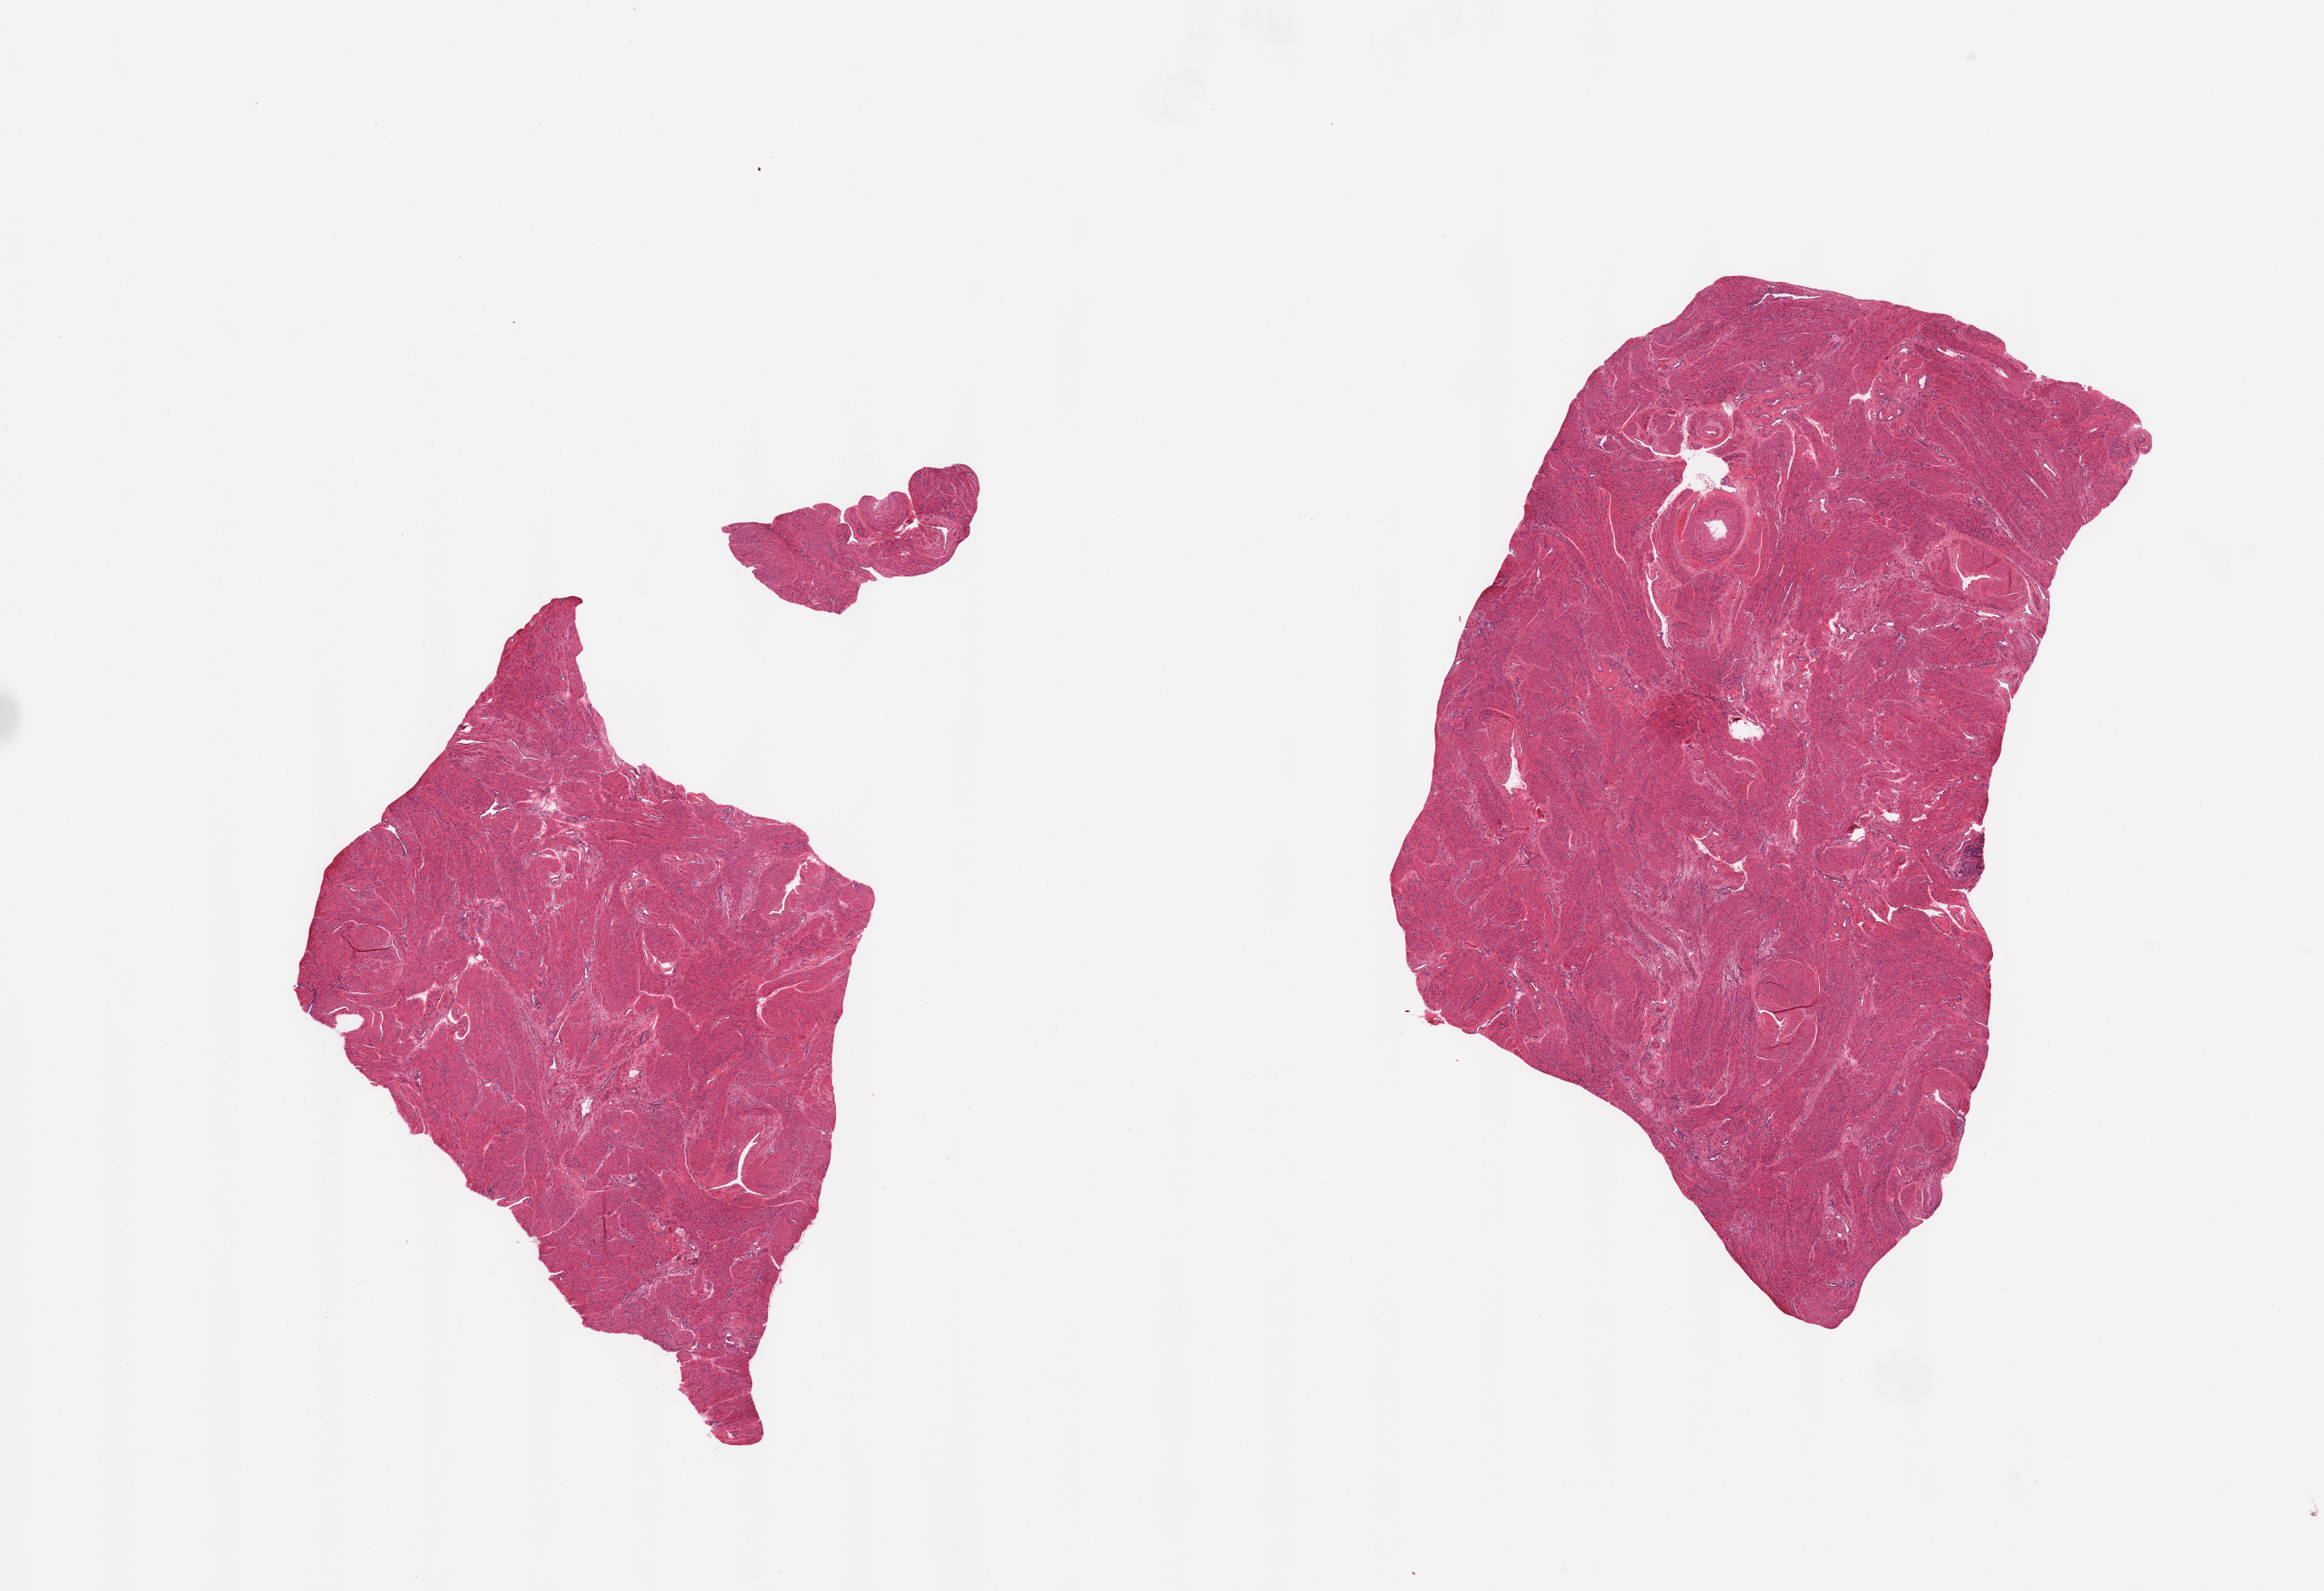
Whole-slide image, hematoxylin and eosin (H&E) stain, brightfield, whole scanned area (about 21.7 x 14.8 mm, from a 20x scan) shown as a low-resolution overview; PAXgene-fixed, paraffin-embedded tissue; section of uterus (target tissue); donor tissue sample. Donor sex: female.
* reviewer comment on this tissue sample: 2 pieces, myometrium, no abnormalities